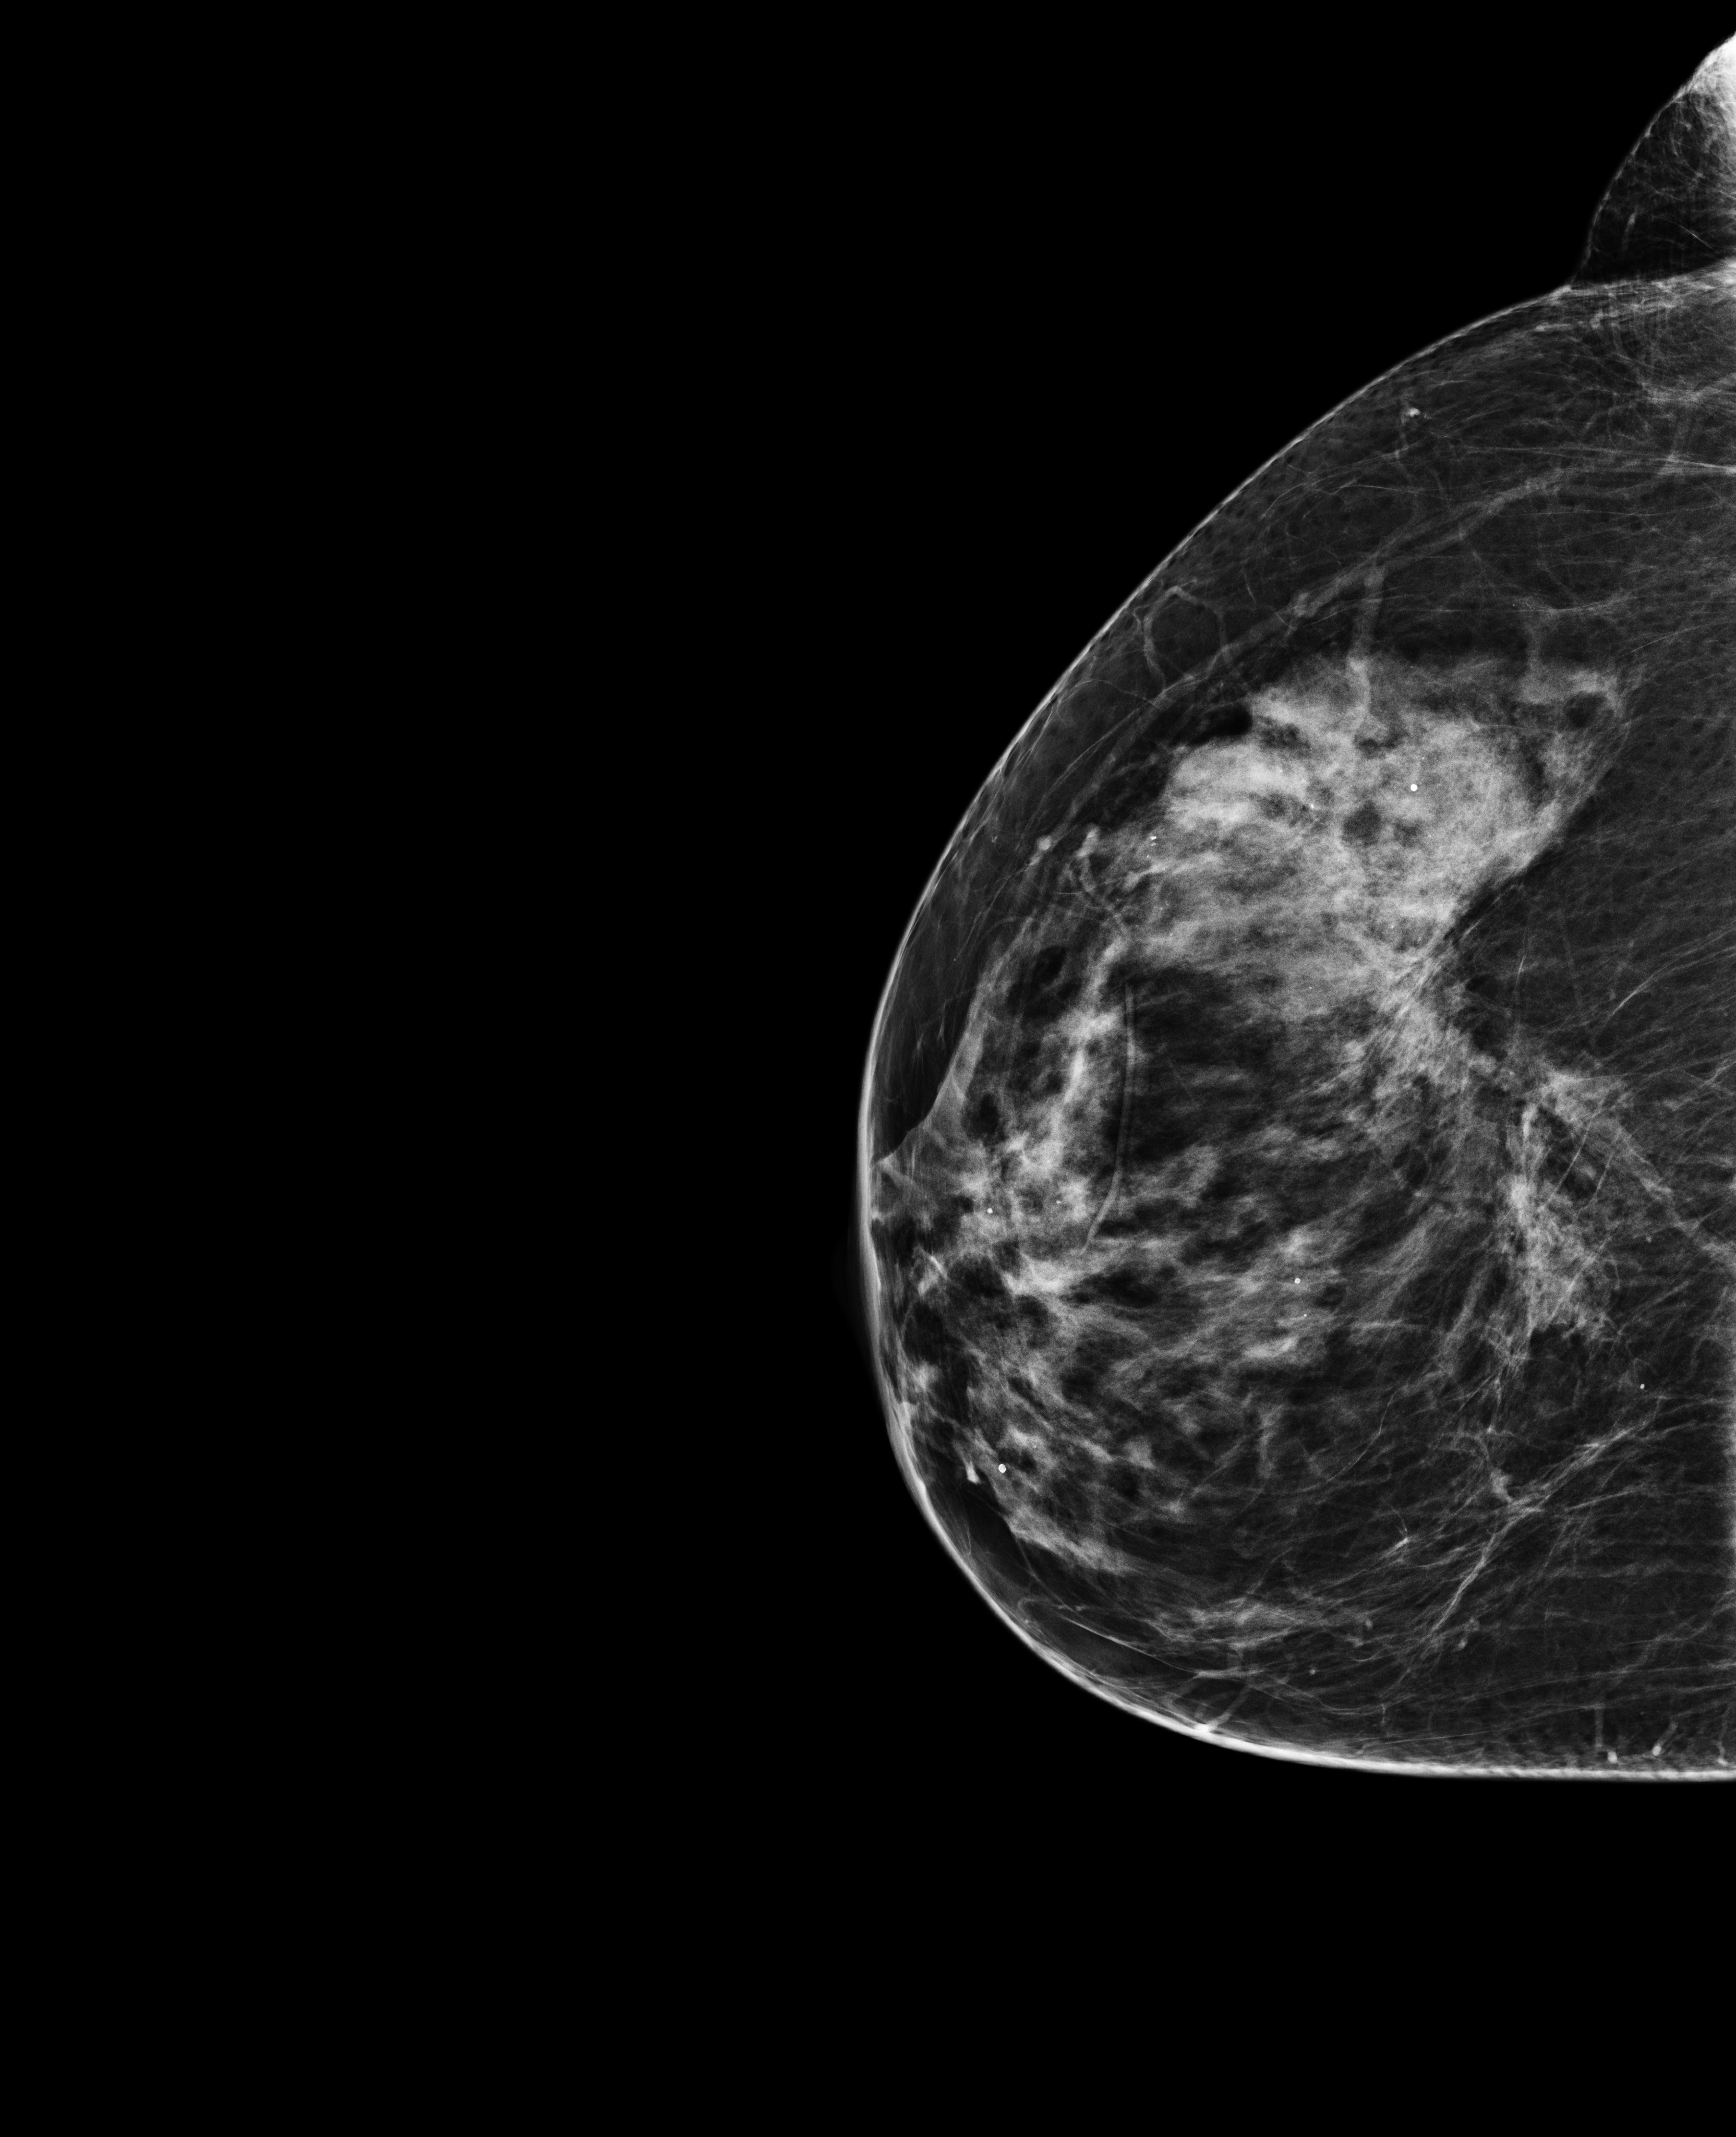
Digital mammogram (FFDM), right breast, laterally exaggerated craniocaudal (XCCL) view, annual screening mammography examination, compressed breast thickness 65 mm. Patient: female, 59 years.
BI-RADS breast density category at the screening exam (both breasts, scale 1–4): 3. Final BI-RADS assessment for this screening round (tomosynthesis exam, both breasts): category 2. Recall: no recall after this screen.